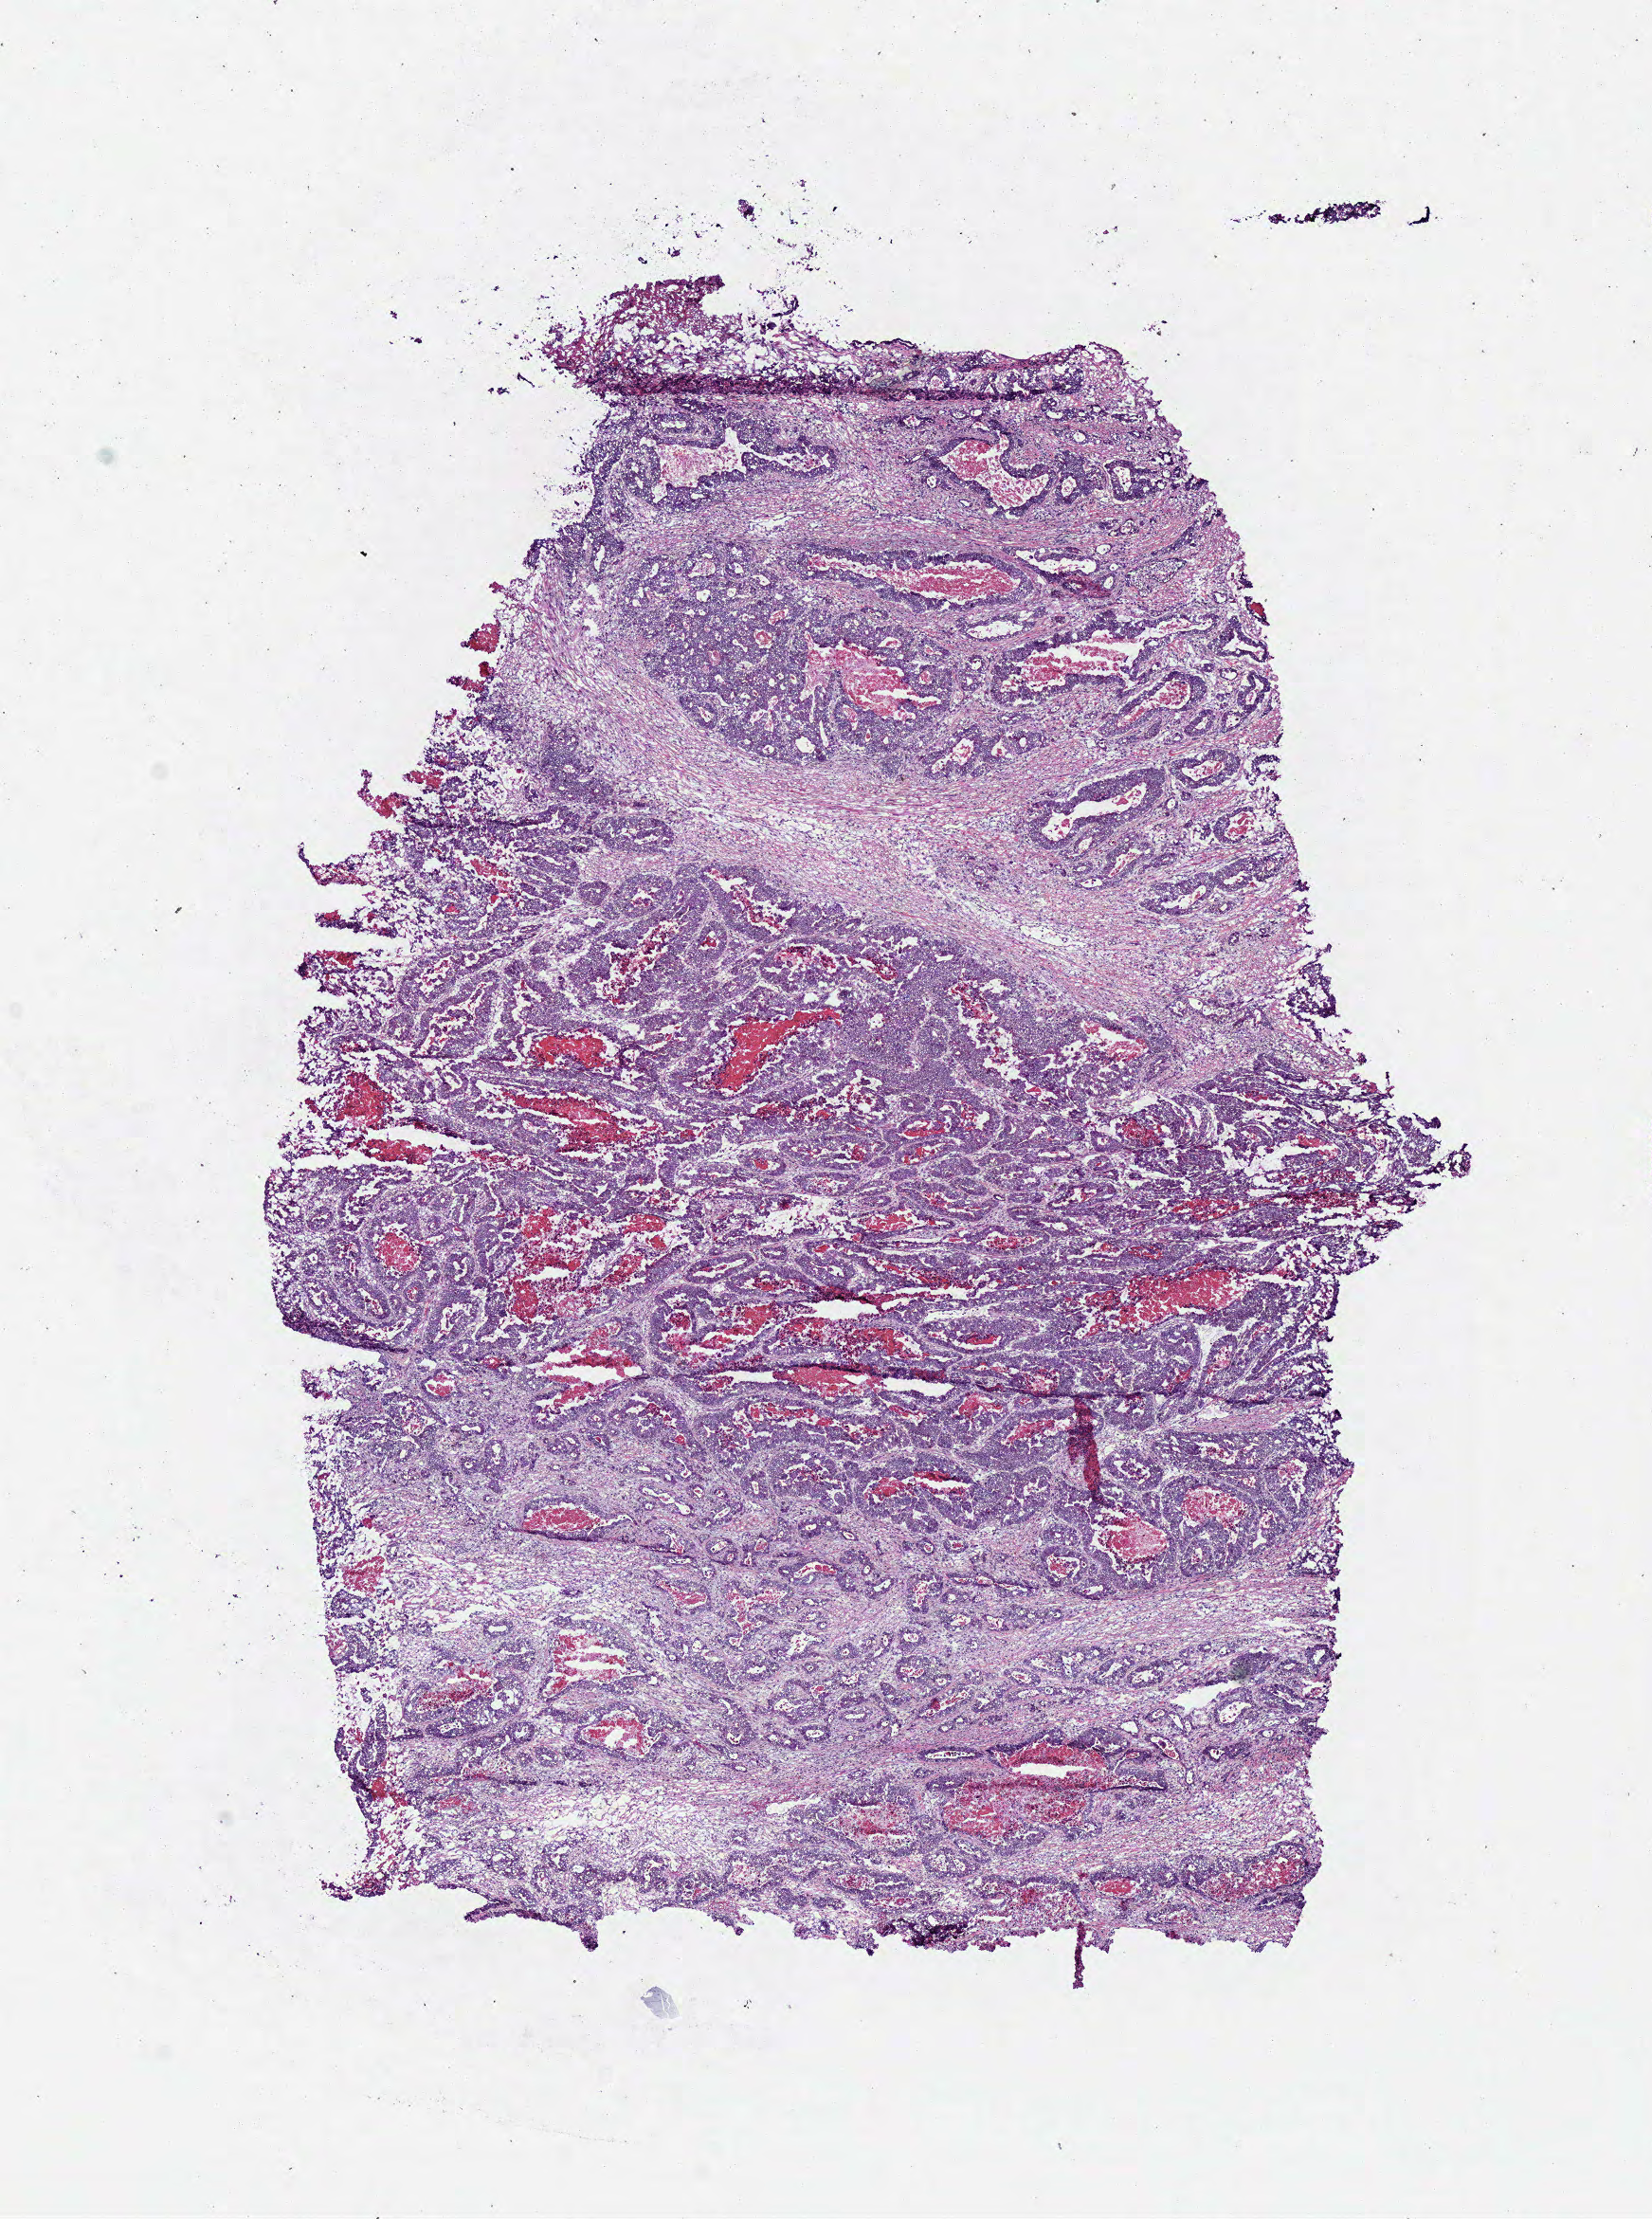
Whole-slide histology image, Hematoxylin and eosin (H&E) stained, whole scanned area (about 6.9 x 9.2 mm, acquisition: 40x scan) shown as a low-resolution overview. Frozen section from the bottom of the tissue portion. Sample: primary tumour, stomach. Patient: female, age at initial diagnosis 70 years. Composition of this section per pathologist review: tumour cells 55%, tumour nuclei 80%.
Histologic diagnosis: Tubular adenocarcinoma (body of stomach).